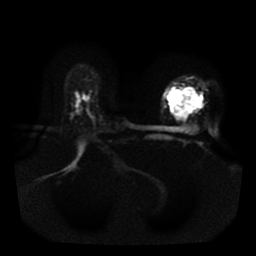
Breast MRI, one axial slice; diffusion-weighted series; image 2 of 4 stored at this slice position (different b-values; order by instance number); 1.5 T; 5 mm slice thickness; 256 × 256 image matrix, field of view 330 × 330 mm. Female patient.
Outlined on this slice (outlined manually by an expert reader):
- tumour on diffusion-weighted imaging: bounding box [x1, y1, x2, y2] px = [168, 89, 203, 120]